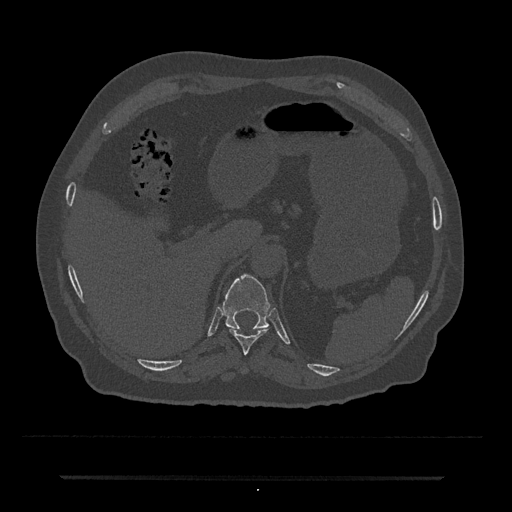
CT including the spine, one axial slice. Slice 204 of 797 in the series (ordered by position). Reconstruction kernel Br40s/3. 120 kVp. Bone window (W 1800 / L 400 HU). 0.5 mm slice thickness. 512 × 512 image matrix, field of view 437 × 437 mm. Patient: male, 69 years. From the clinical record (not read from this slice): primary cancer: prostate.
Structures marked on this image (semi-automatic segmentation, software-assisted and operator-edited):
- T10 vertebra: bounding box <229,329,267,355> (left, top, right, bottom; pixels)
- T11 vertebra: <222,274,270,330>